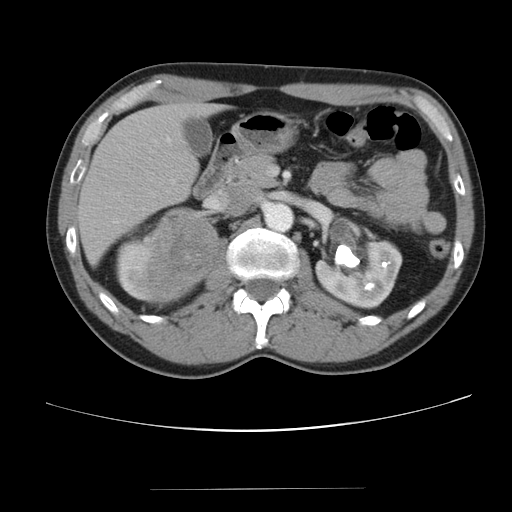
Contrast-enhanced abdominal CT, one axial slice; slice 59 of 80 in the series (ordered by position); reconstruction kernel STANDARD; soft-tissue window (W 400 / L 40 HU); 512 × 512 image matrix, field of view 360 × 360 mm. Patient: male, 61 years. Case-level facts recorded for this patient, not image findings: diagnosis: adrenocortical carcinoma; tumour side: right adrenal; tumour size at pathology: 11.1 cm; Ki-67 index: 32 %; stage (as recorded): 2.
Structures marked on this image (semi-automatically segmented with operator editing):
- mass: box from (x=150, y=210) to (x=216, y=298) px